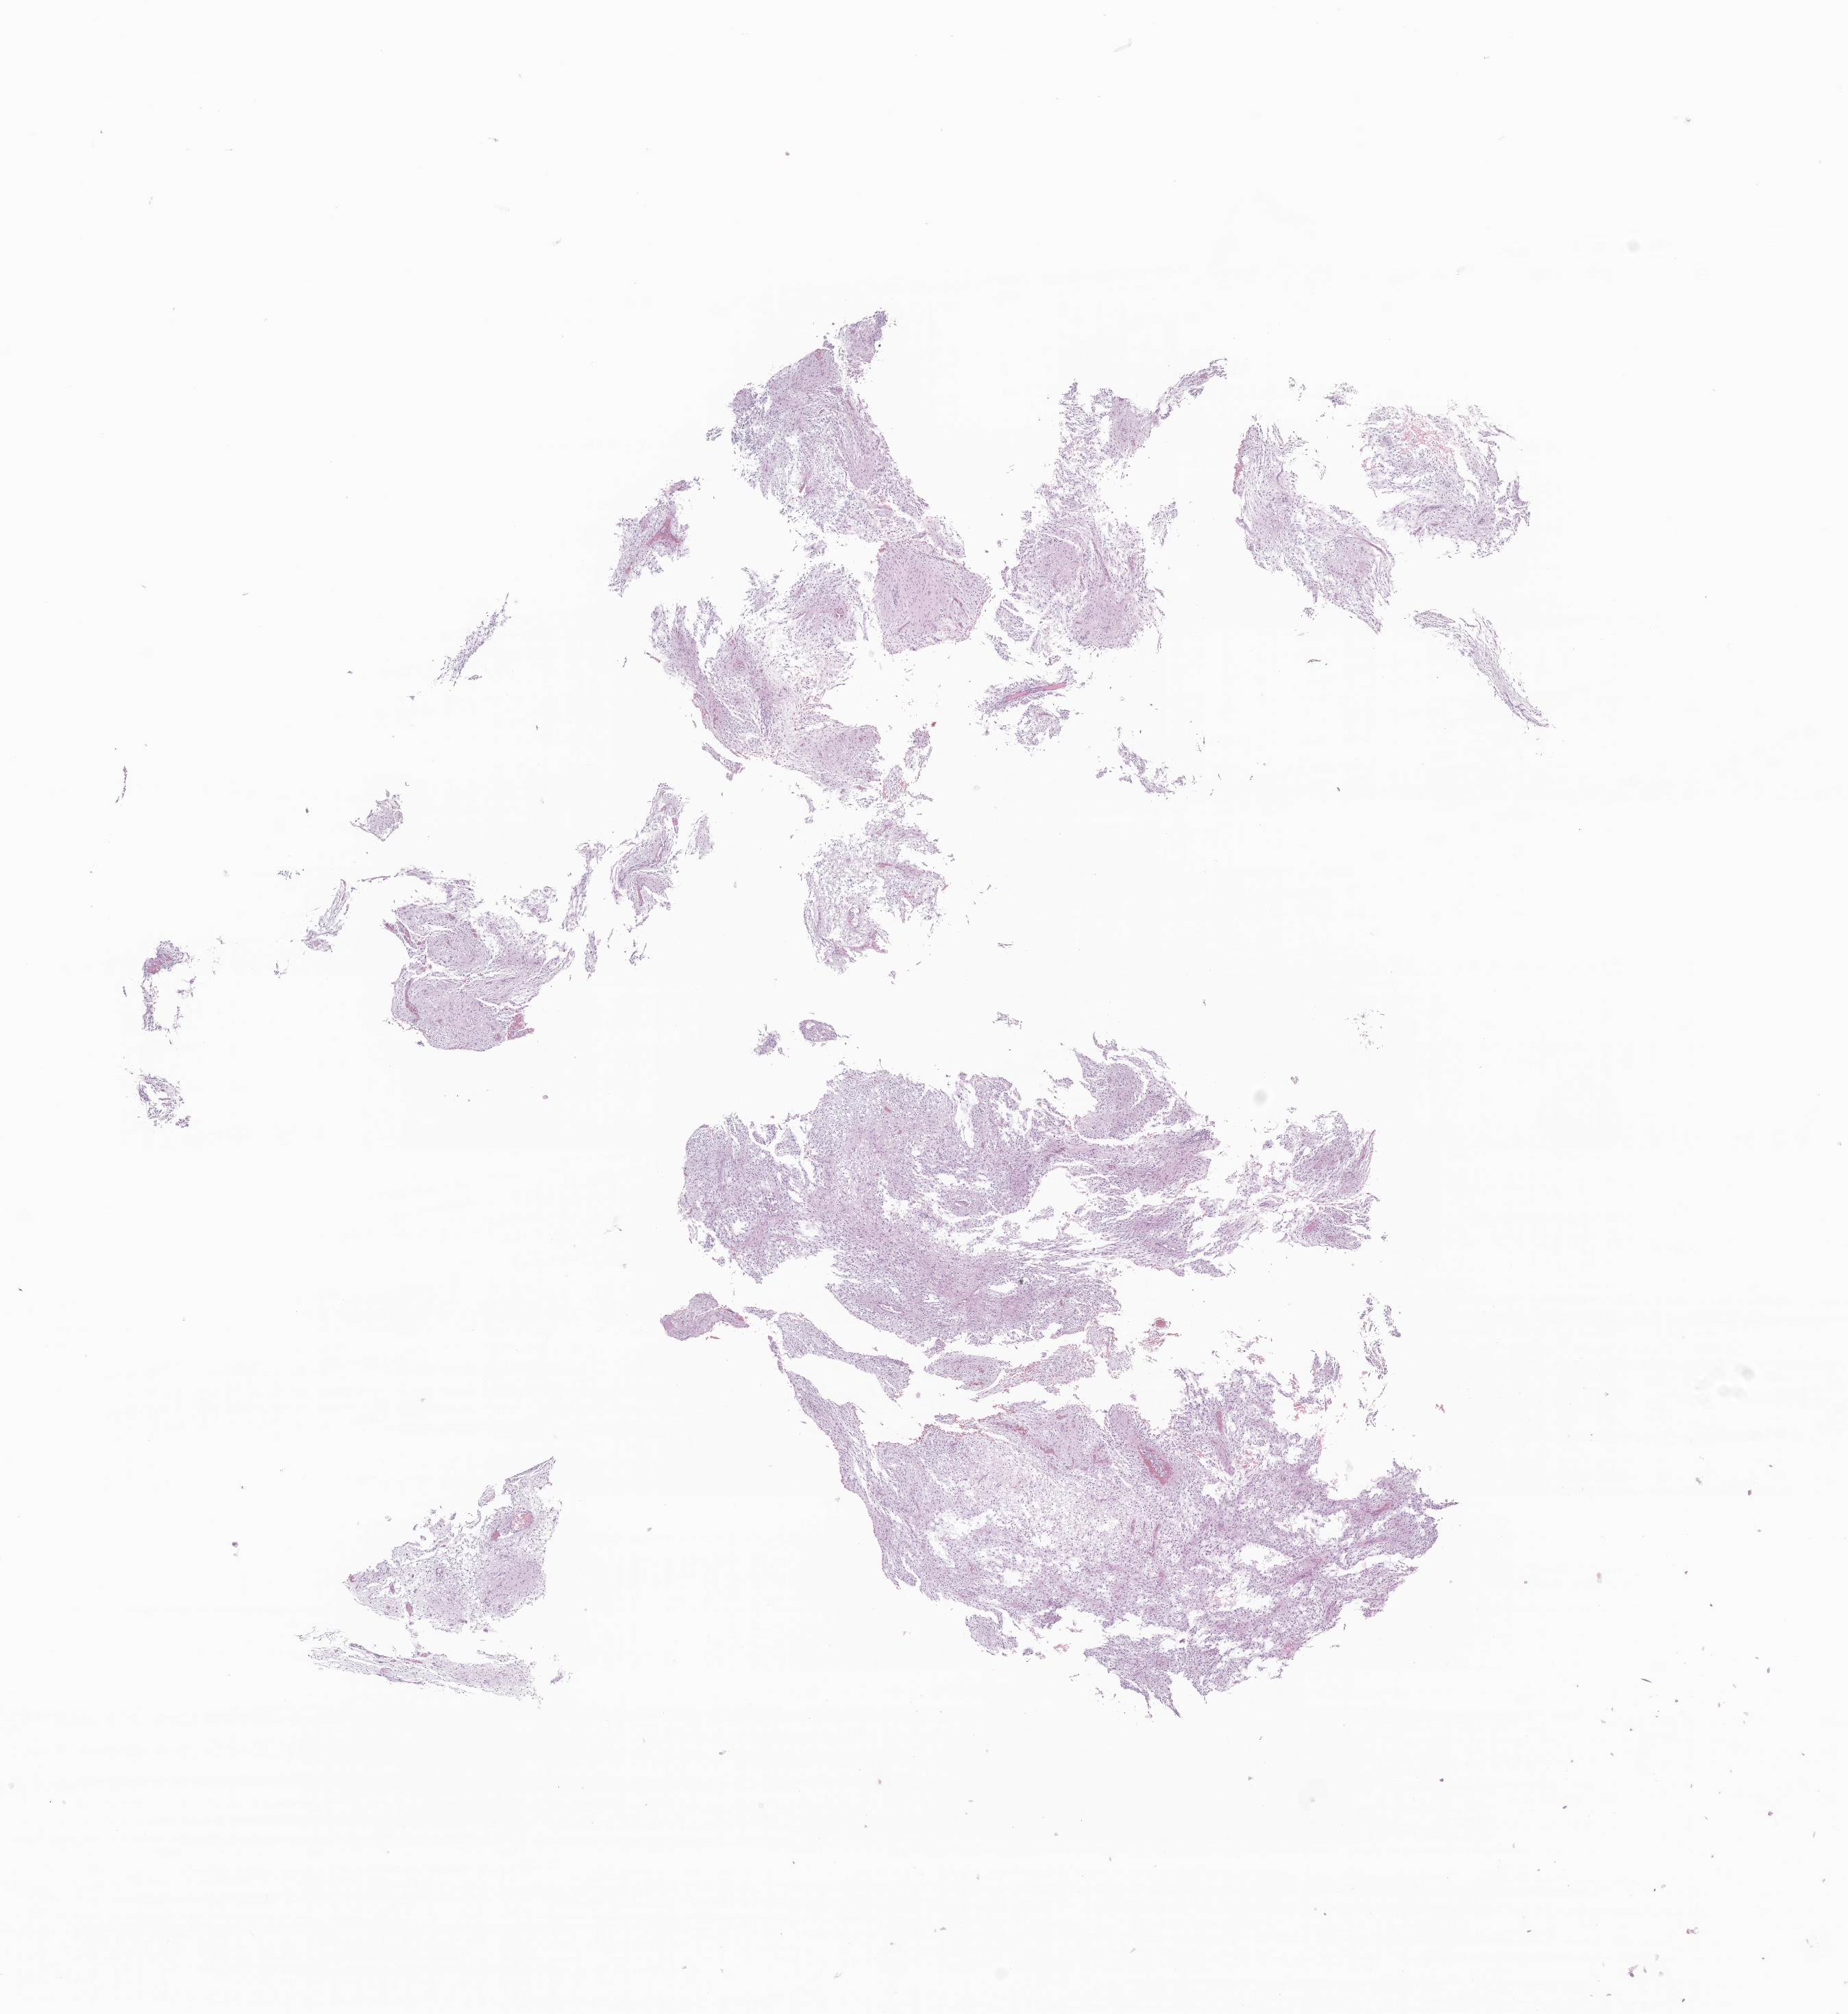
Whole-slide image, hematoxylin and eosin (H&E) stain of tumor tissue from the cerebrum — whole scanned area (about 11.4 x 12.4 mm) shown as a low-resolution overview, formalin-fixed, paraffin-embedded (FFPE) tissue. Female patient, age 823 days (about 2.3 years).
Recorded diagnosis: Tumor cells, uncertain whether benign or malignant.